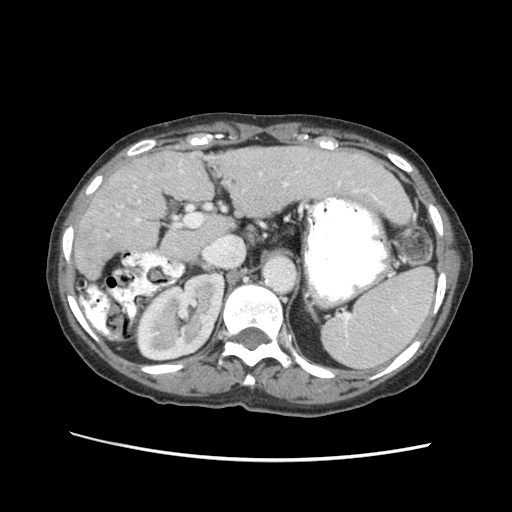
Contrast-enhanced abdominal CT (liver protocol), one axial slice; position 35 of 63 along the scan axis; reconstruction kernel STANDARD; 120 kVp; soft-tissue window (W 400 / L 40 HU); 512 × 512 image matrix, field of view 340 × 340 mm. From the clinical record (not read from this slice): diagnosis: hepatocellular carcinoma (patient treated with transarterial chemoembolisation; whether this scan precedes or follows treatment is not stated here); TNM stage (as recorded): Stage-I; Child-Pugh class: B; tumour differentiation: well differentiated; tumour nodularity: uninodular.
Structures marked on this image (semi-automatic segmentation, software-assisted and operator-edited):
- abdominal aorta: box from (x=265, y=257) to (x=294, y=291) px
- liver parenchyma outside the tumour (the mass and vessels are separate outlines, so this box may not span the whole liver): (x=74, y=142)–(x=404, y=282)
- liver vessels: (x=107, y=170)–(x=369, y=237)